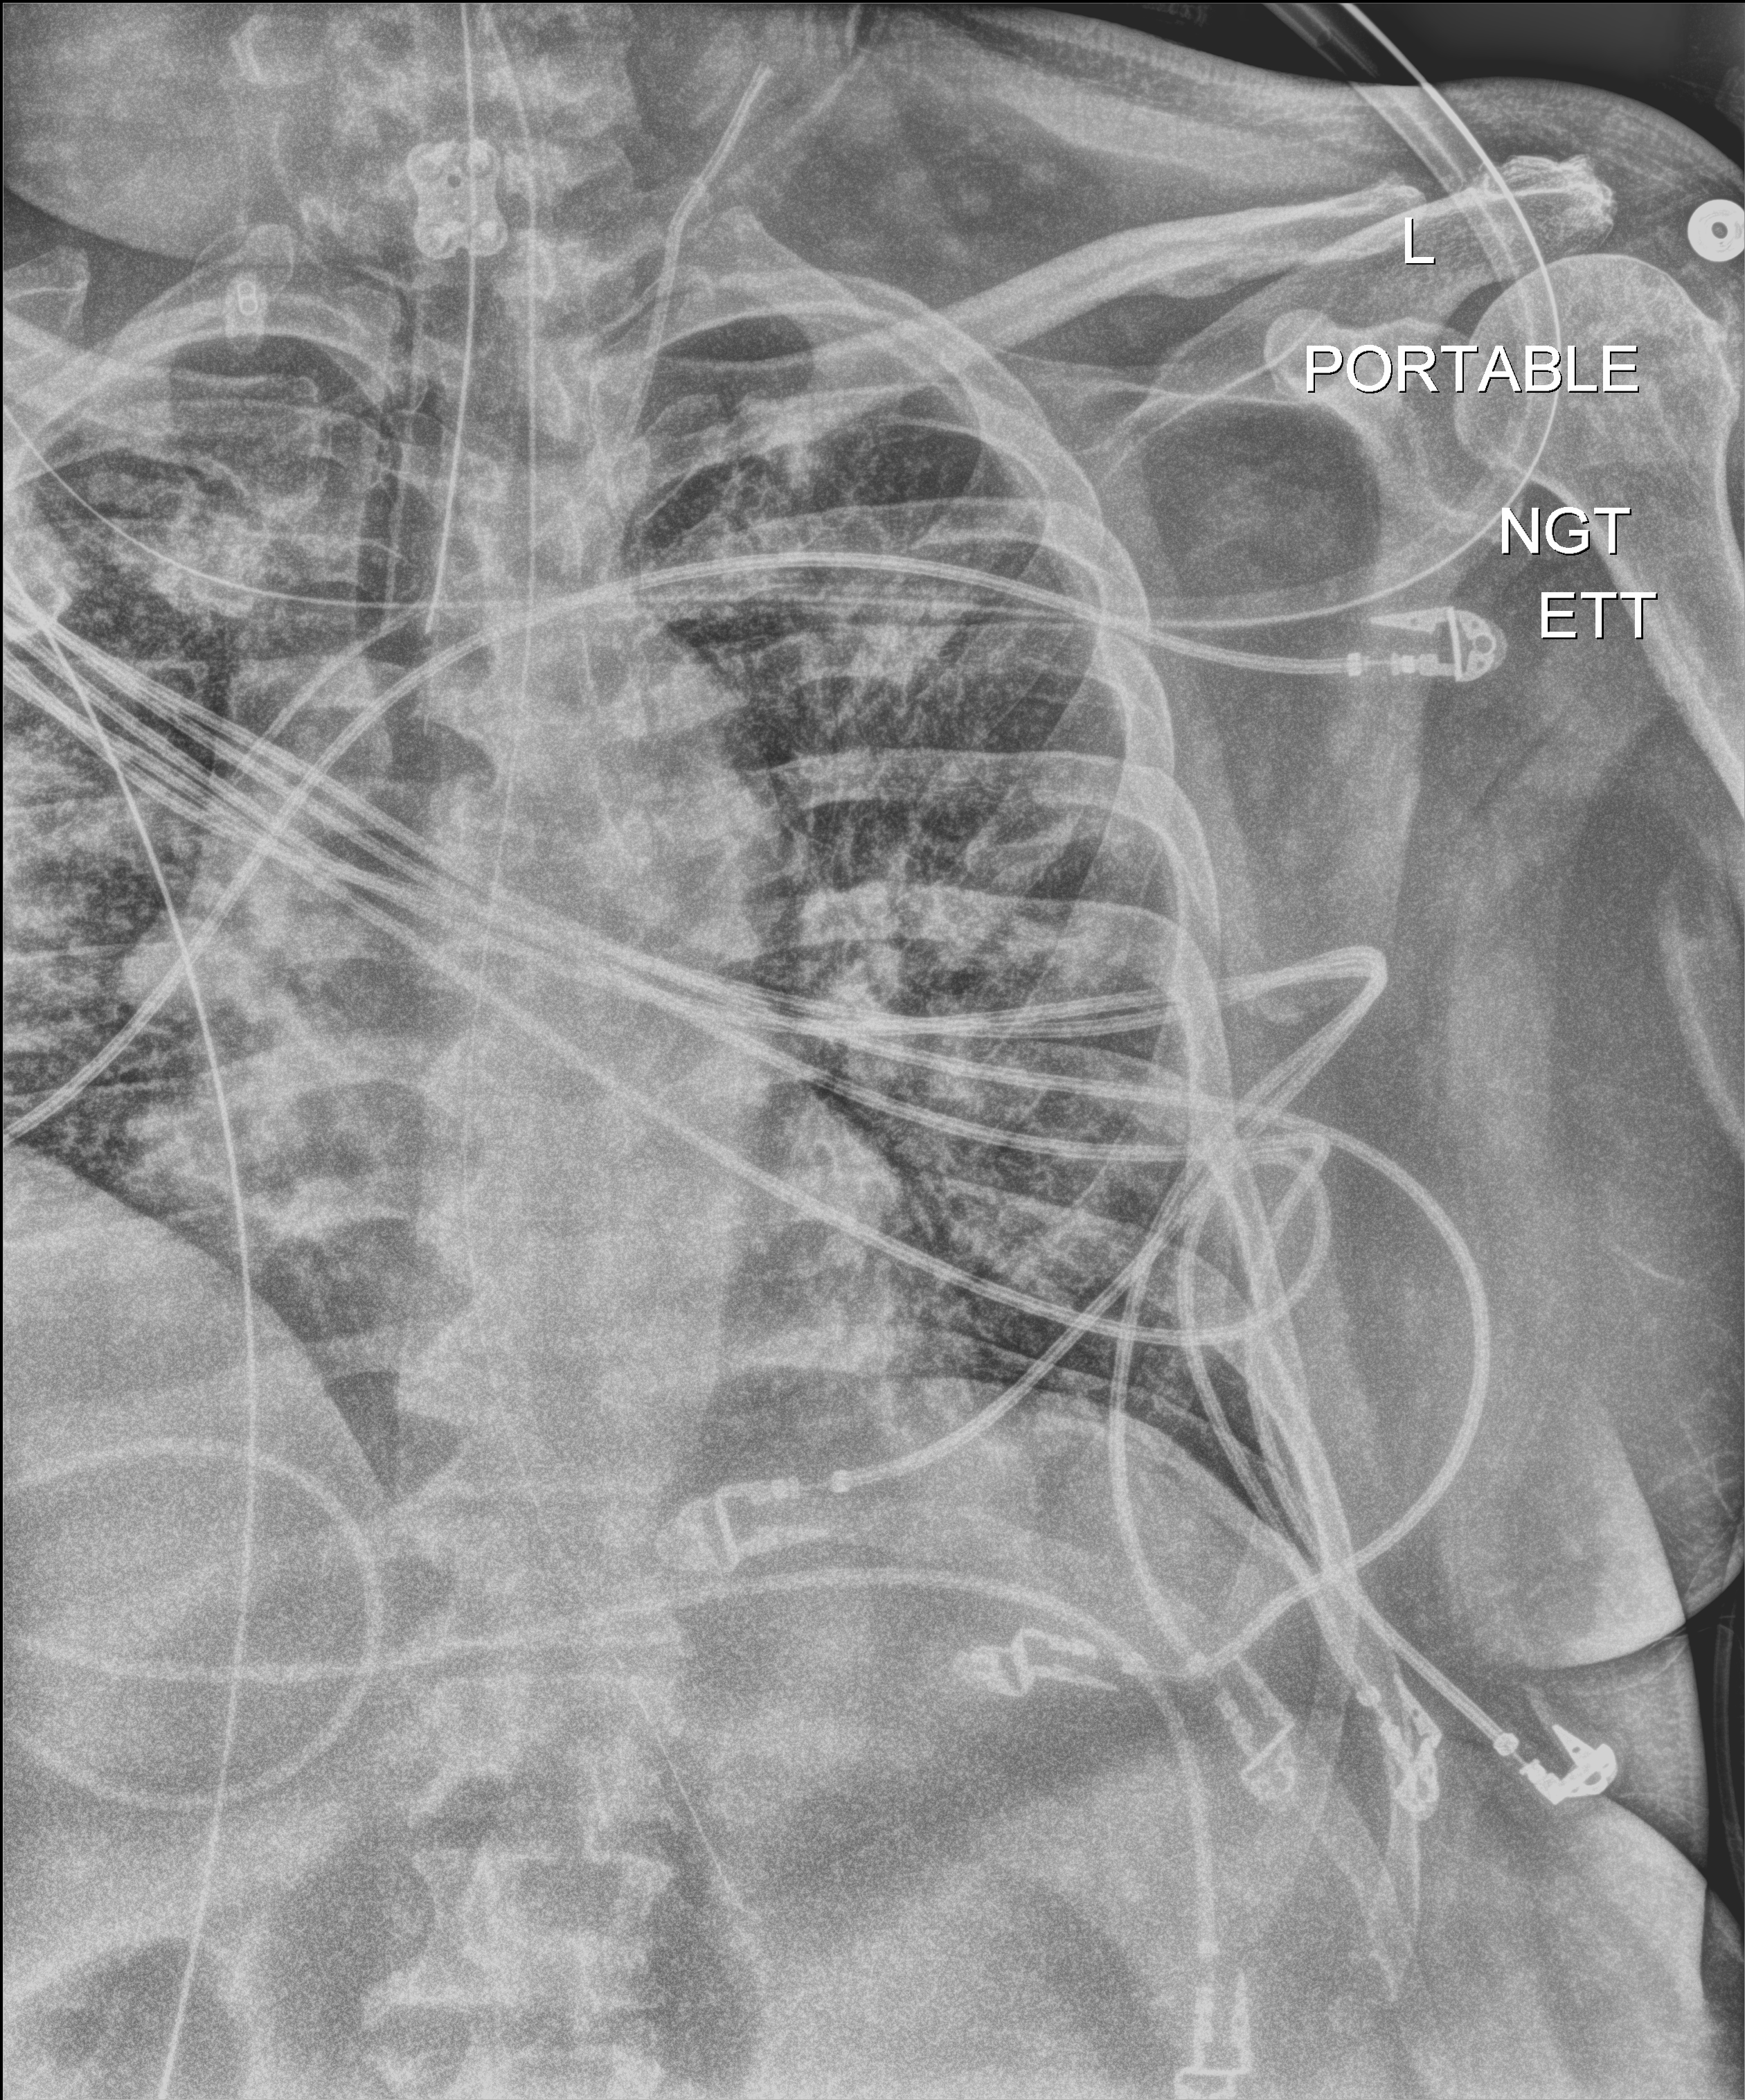
Chest X-ray (portable); anteroposterior (AP) projection. Male patient hospitalised with COVID-19, age 18–59 years.
Hospital-stay facts (about this admission, not read from this image; timing relative to this image not recorded): mechanically ventilated during this hospital stay: yes; admitted to intensive care during this hospital stay: yes.